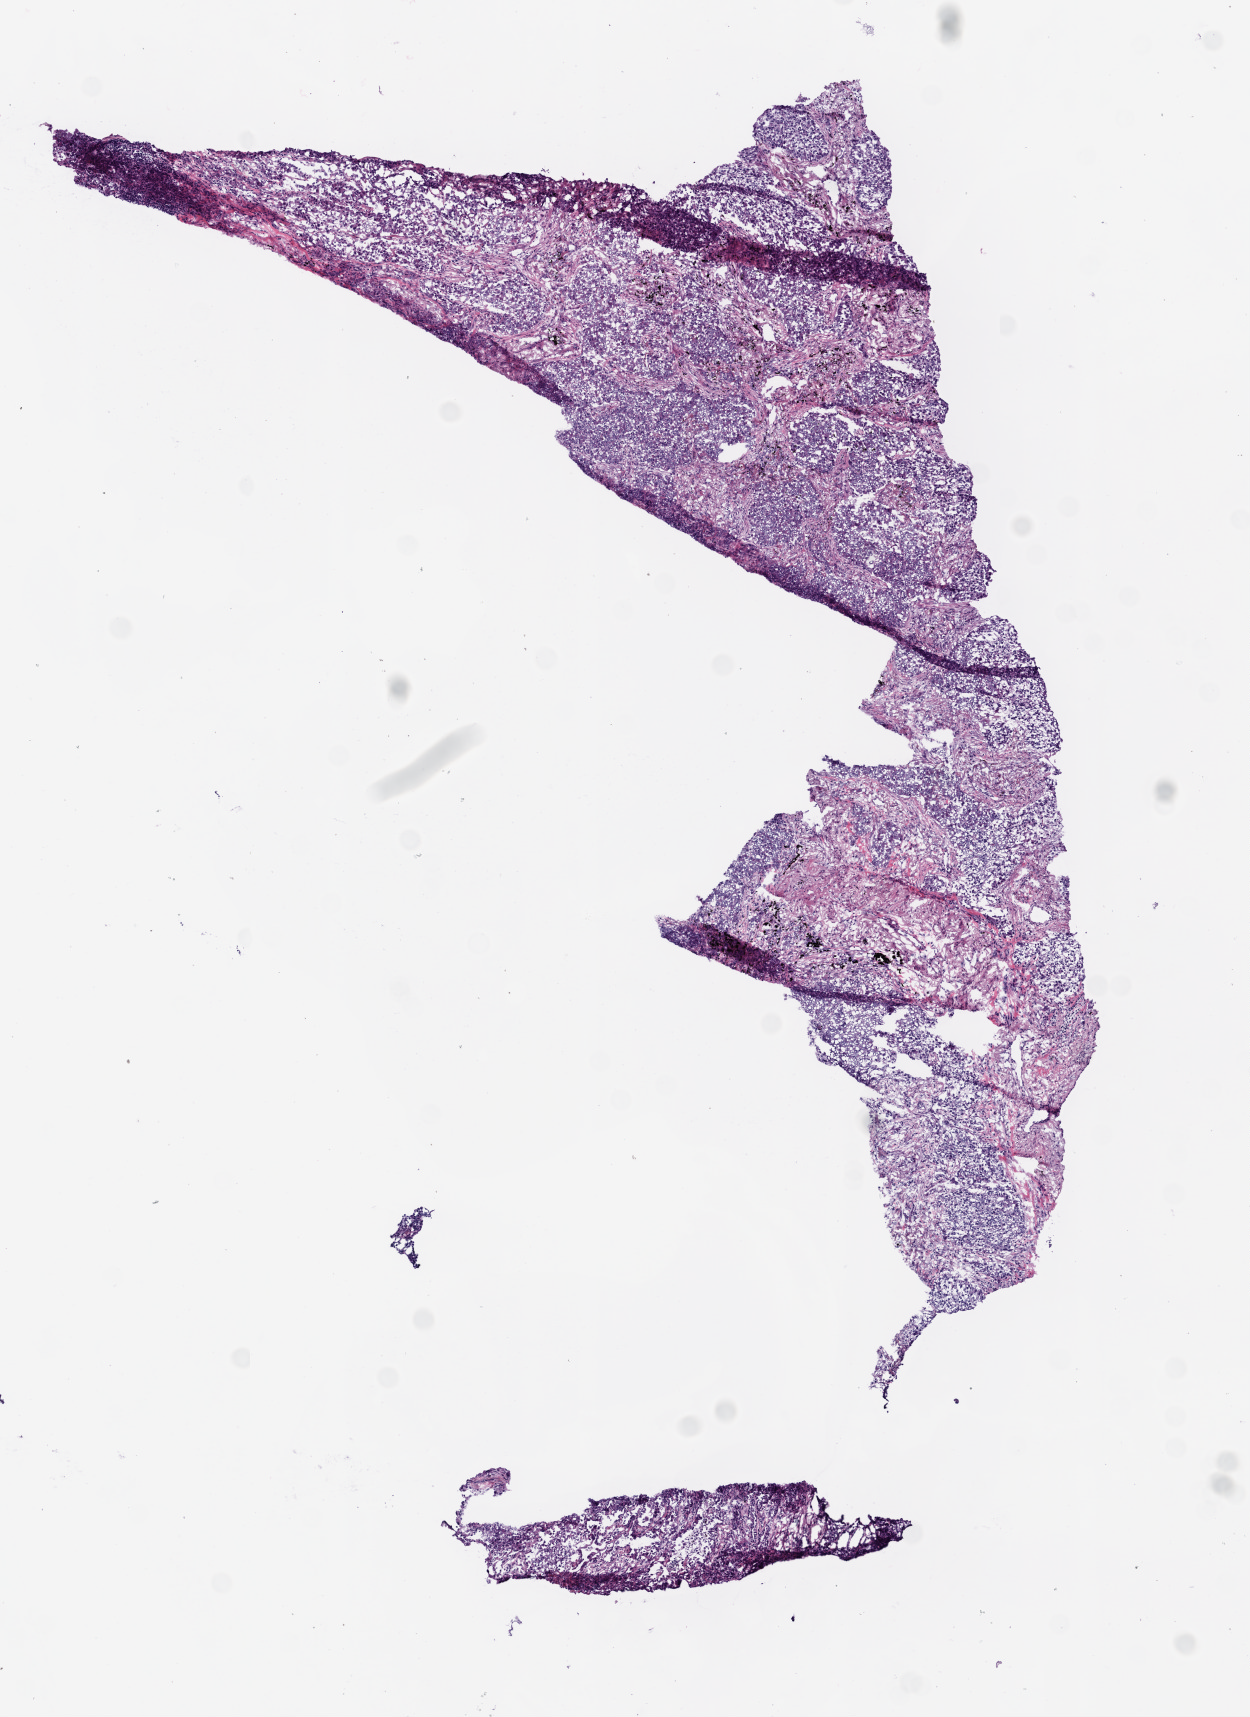
Digitized Hematoxylin and eosin (H&E) stained tissue section (whole slide) — low-resolution overview of the scanned area, about 5.0 x 6.9 mm (slide scanned at 20x), frozen section from the bottom of the tissue portion, sample: primary tumour, lung. Patient: female, age at initial diagnosis 74 years. Slide review estimates, as recorded: tumour cells 90%, tumour nuclei 90%.
Histologic diagnosis: Clear cell adenocarcinoma, NOS (lower lobe, lung).